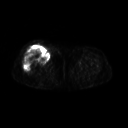
FDG PET of an extremity soft-tissue mass (from a PET/CT study), one axial slice. Slice 244 of 311 in the series (ordered by position). 3.27 mm slice thickness. 128 × 128 image matrix, field of view 500 × 500 mm. Female patient, age 57 years. Case-level facts recorded for this patient, not image findings: histological type: pleiomorphic undifferentiated sarcoma; grade: high; site of the primary tumour: right quadricep.
Annotated regions visible in this slice (expert contour drawn on MRI and transferred to this co-registered scan by the dataset authors):
- tumour plus oedema (research contour): box from (x=24, y=47) to (x=49, y=71) px
- tumour (research contour): (x=24, y=47)–(x=49, y=71)